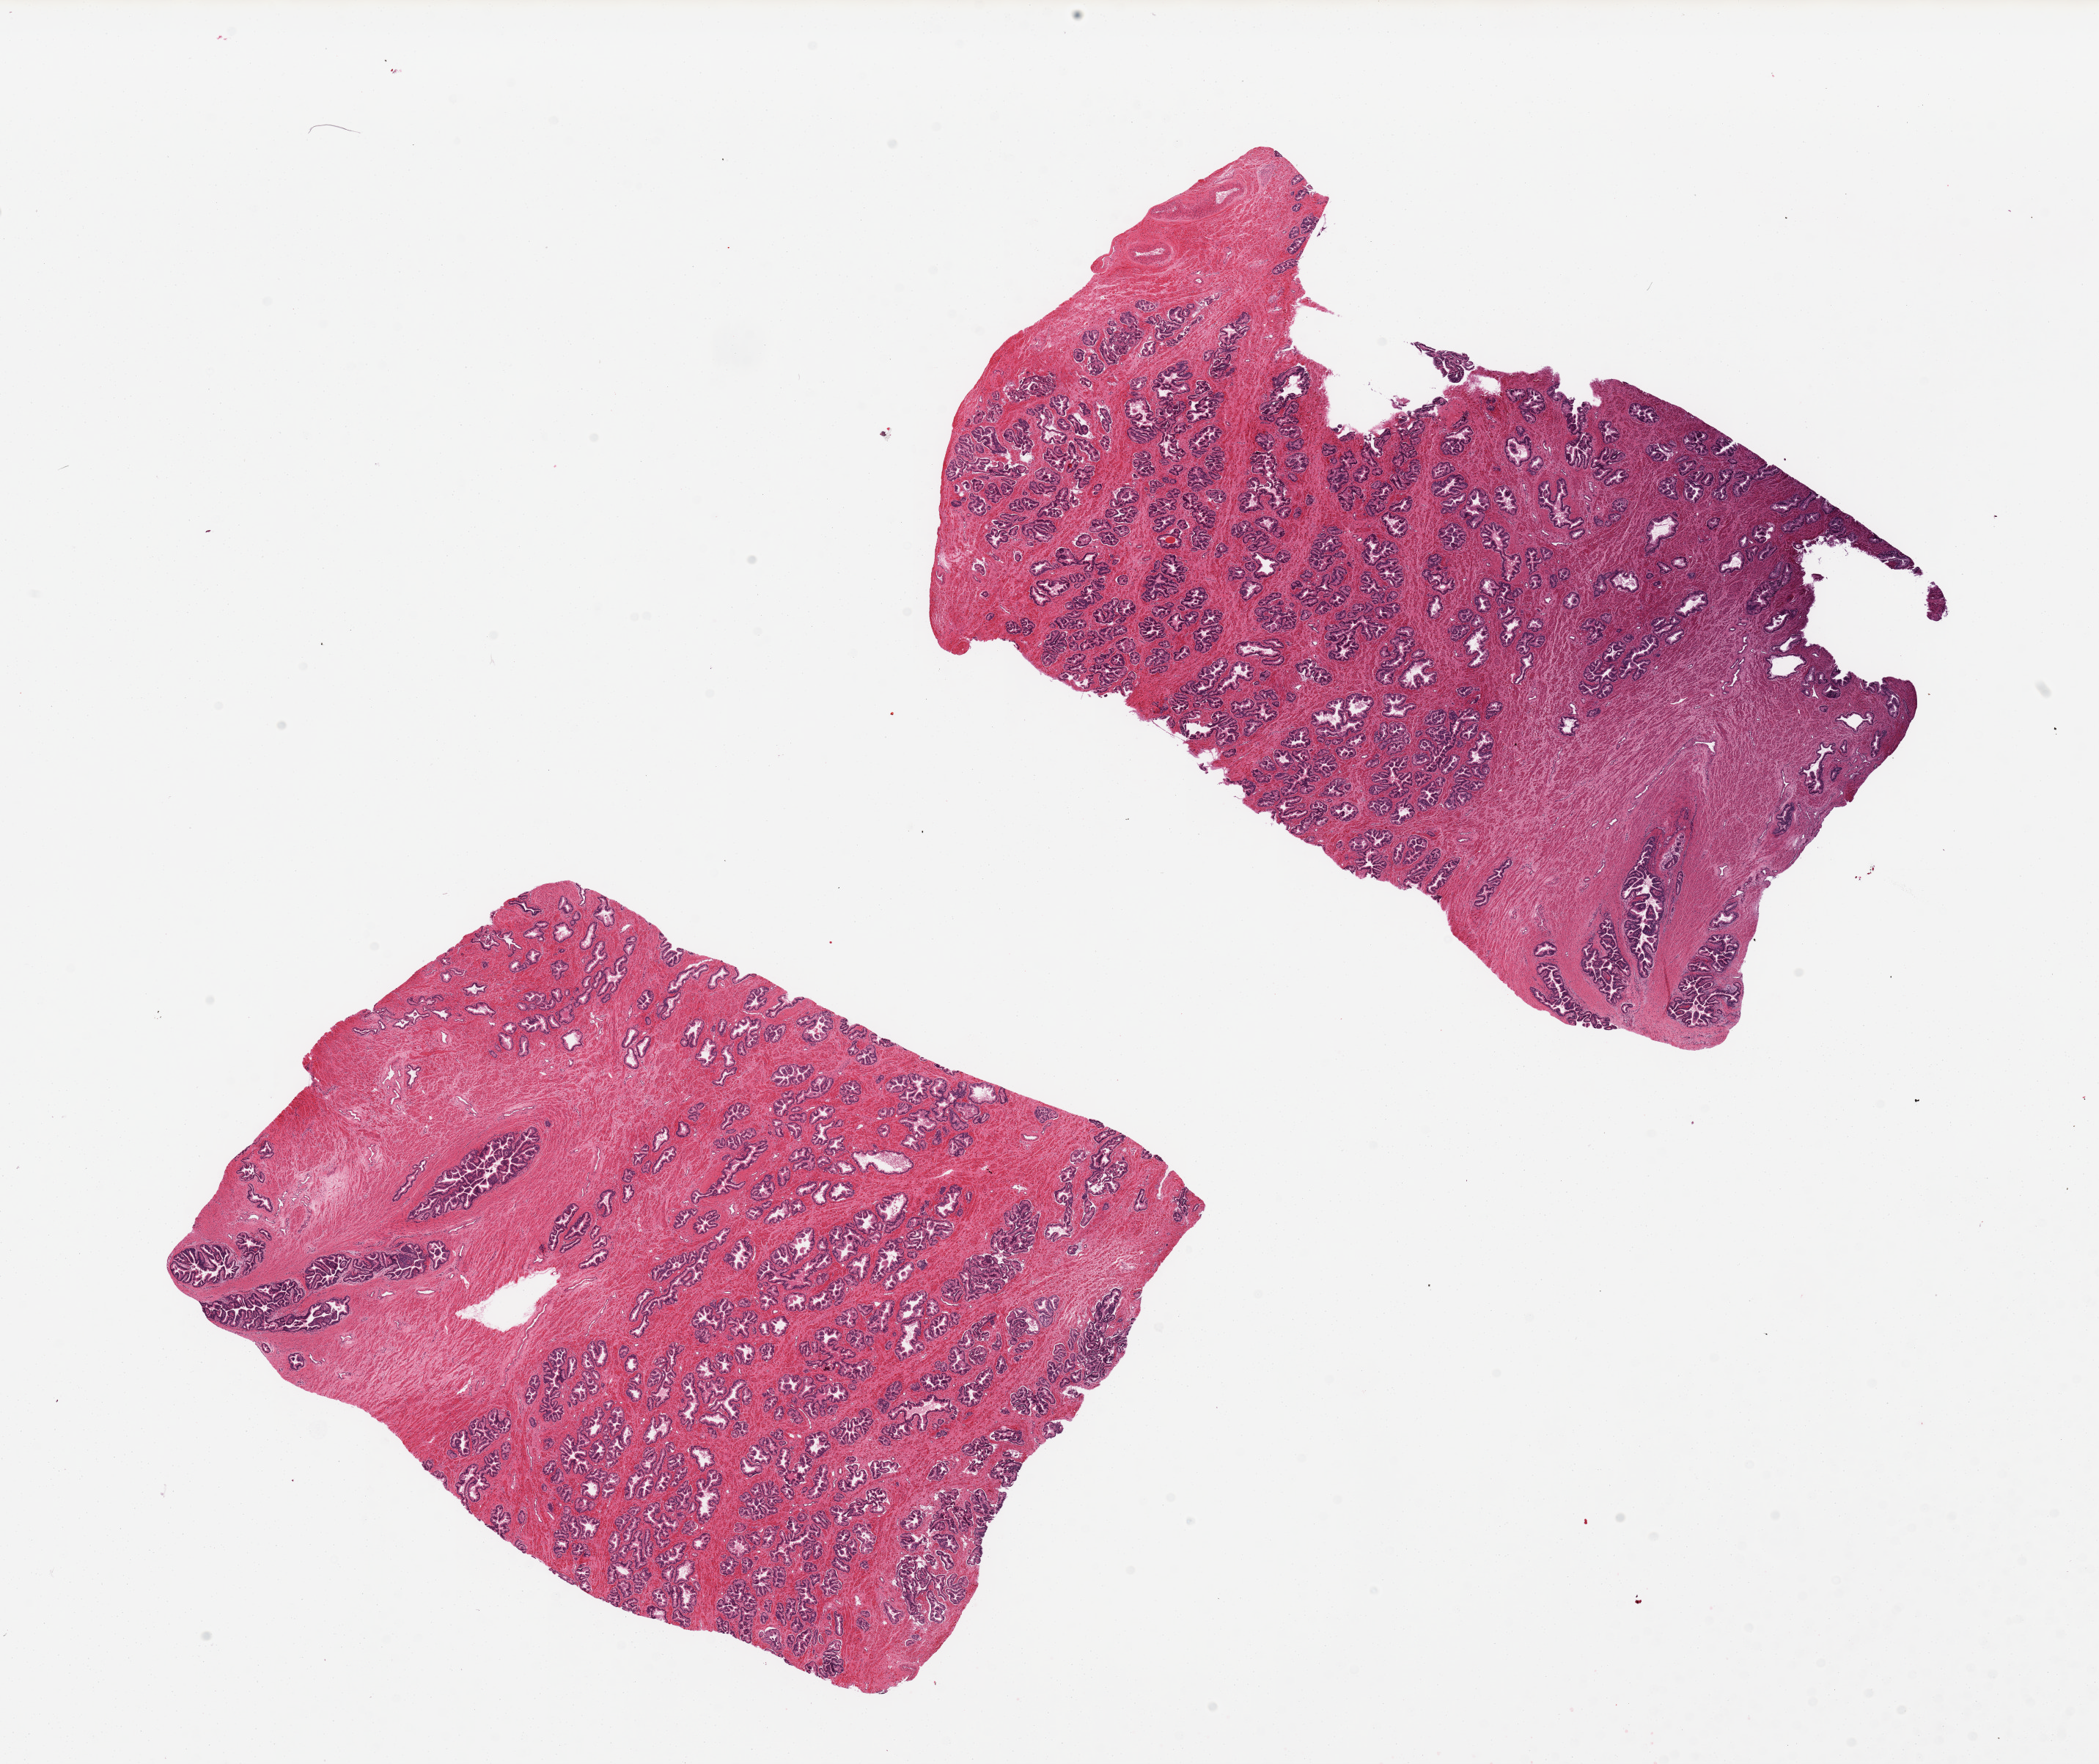
Whole-slide image, H&E stain — a low-resolution overview of the entire scanned area, about 22.6 x 19.0 mm. PAXgene-fixed, paraffin-embedded tissue. Sampled site (target tissue): prostate. Donor tissue sample. Donor sex: male.
Reviewer comment on this tissue sample: 2 pieces, glandular hyperplastic pattern.